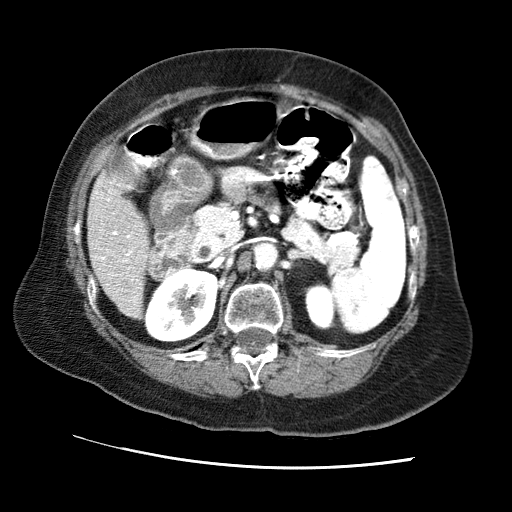
Contrast-enhanced abdominal CT (liver protocol), one axial slice. Position 24 of 65 along the scan axis. Soft-tissue window (W 400 / L 40 HU). 2.5 mm slice thickness. 512 × 512 image matrix, field of view 340 × 340 mm. Case-level facts recorded for this patient, not image findings: diagnosis: hepatocellular carcinoma (patient treated with transarterial chemoembolisation; whether this scan precedes or follows treatment is not stated here); TNM stage (as recorded): Stage-II; Child-Pugh class: A; tumour nodularity: multinodular; tumour size: 2.5 cm.
Structures marked on this image (semi-automatic segmentation, software-assisted and operator-edited):
- liver parenchyma outside the tumour (the mass and vessels are separate outlines, so this box may not span the whole liver): bounding box [x1, y1, x2, y2] px = [86, 177, 148, 318]
- liver vessels: [96, 191, 136, 303]